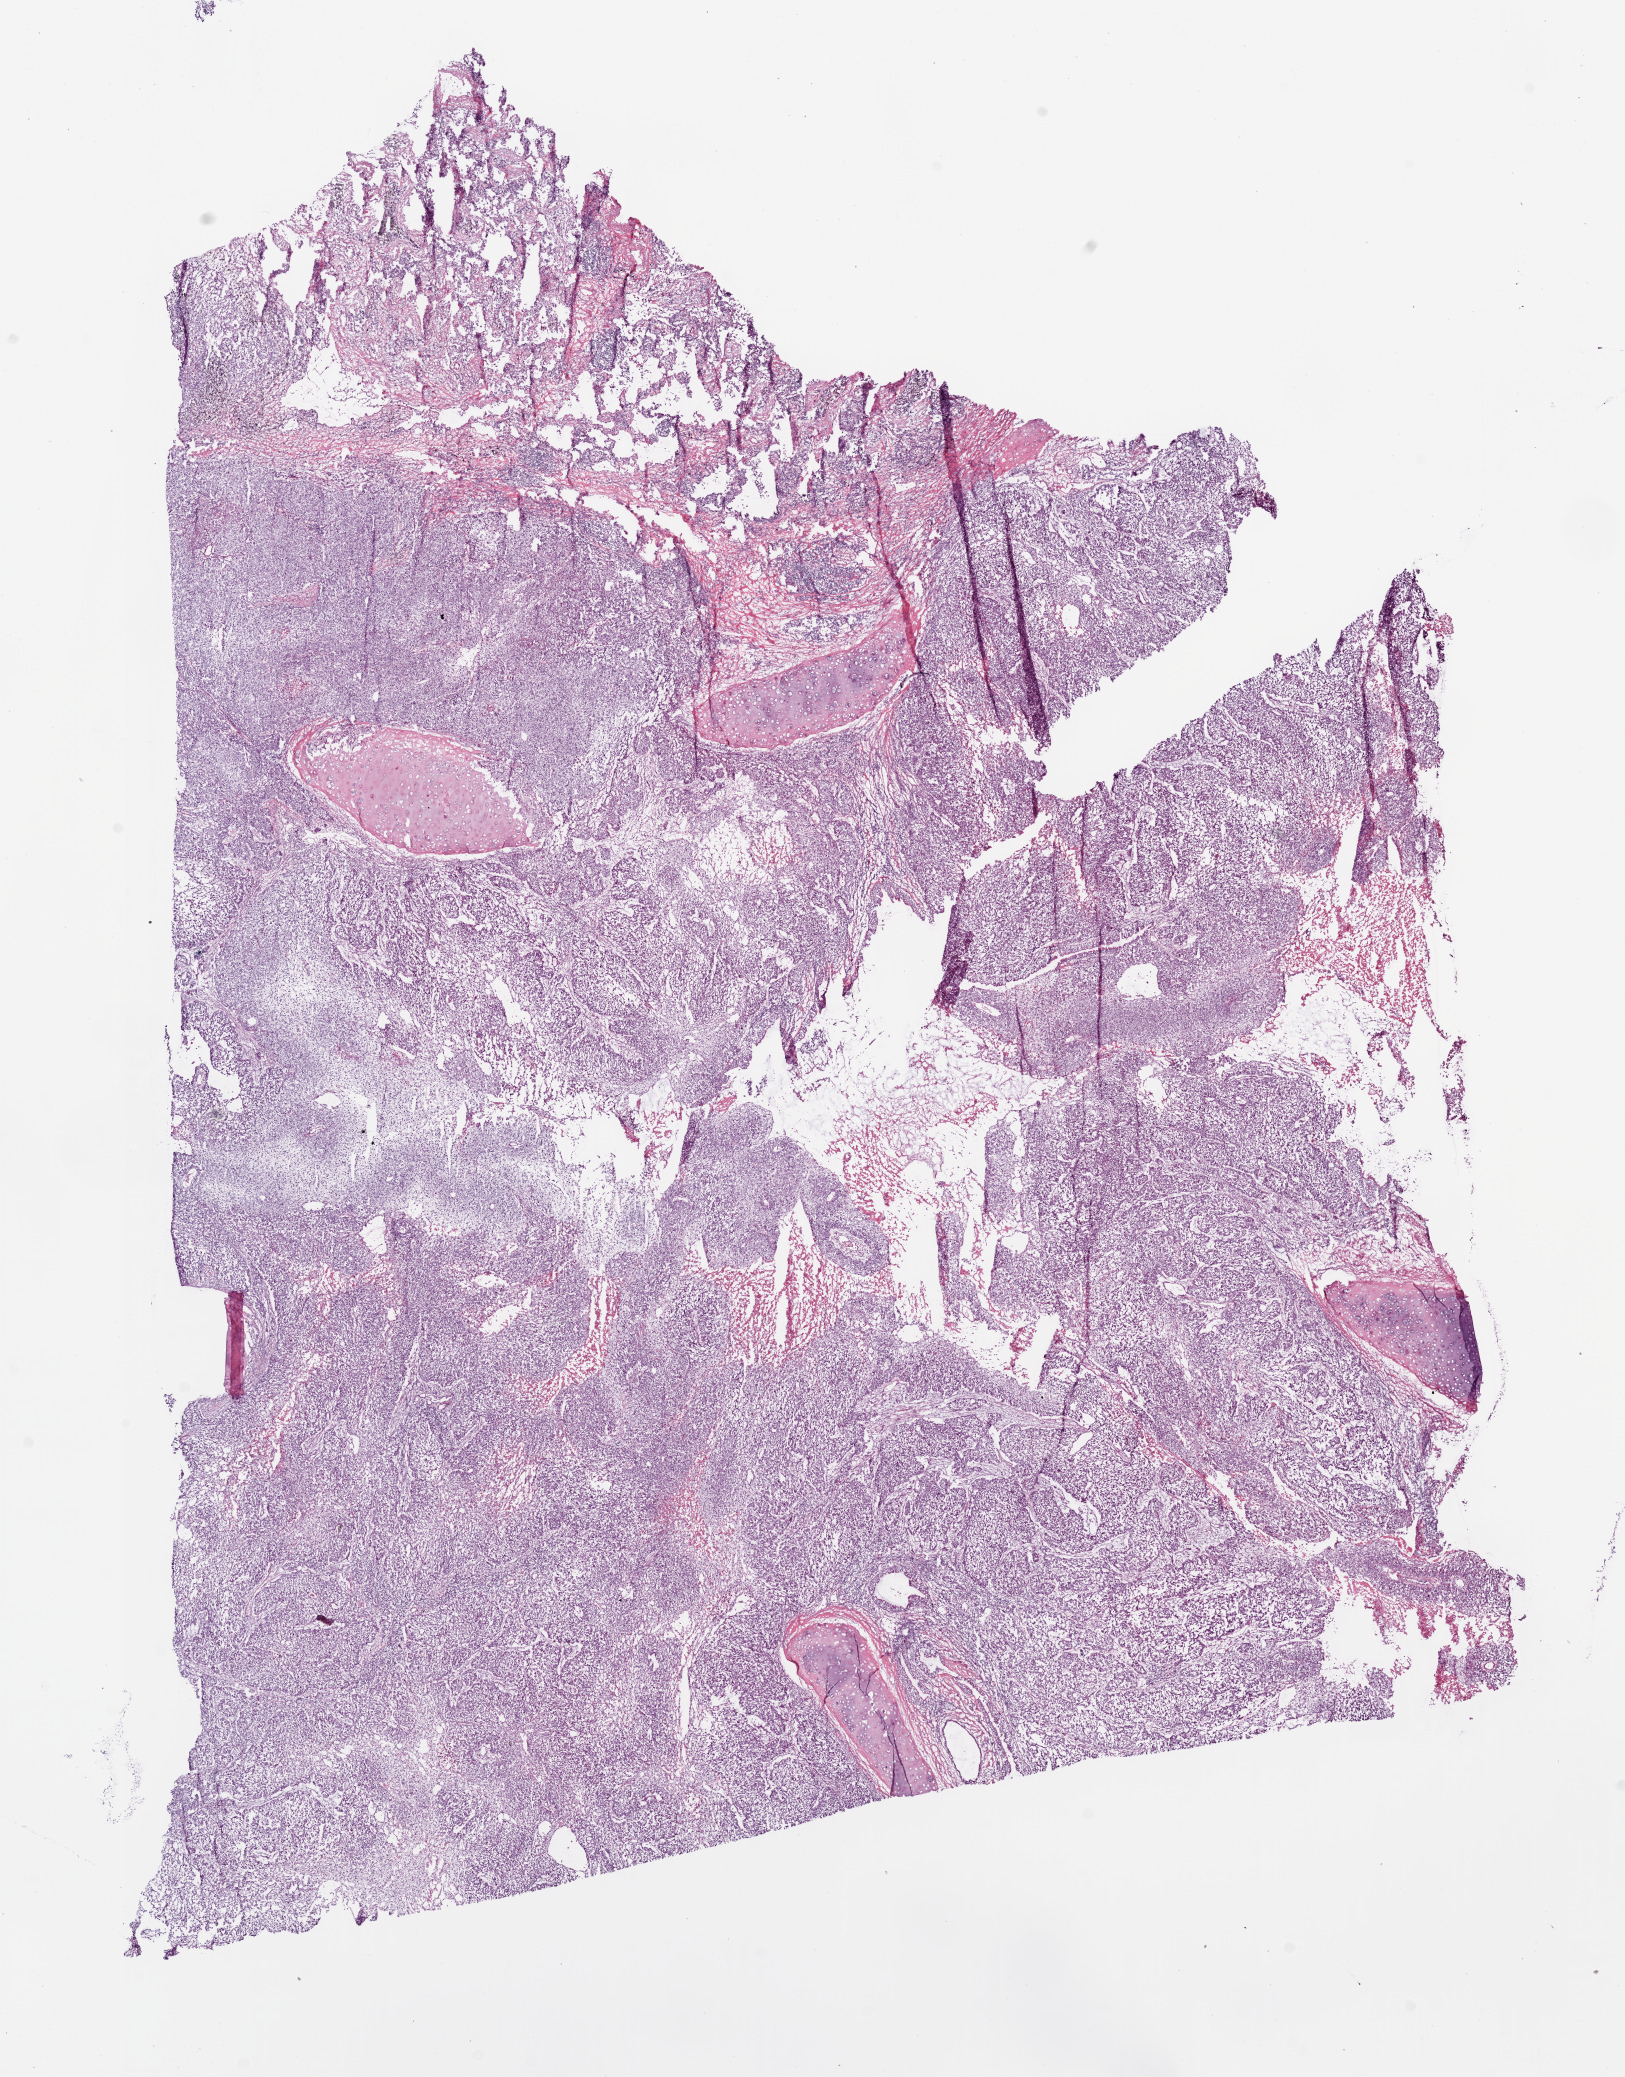
Whole-slide histology image, H&E — whole scanned area (about 13.0 x 16.7 mm) shown as a low-resolution overview; frozen section; lung, primary tumour sample. Male patient; age at initial diagnosis 72 years. Composition of this section per pathologist review: tumour cells 58%, tumour nuclei 75%, normal cells 15%, stromal cells 15%, necrosis 12%.
Pathologic diagnosis: Squamous cell carcinoma, NOS (upper lobe, lung). AJCC pathologic stage: IA (6th edition).